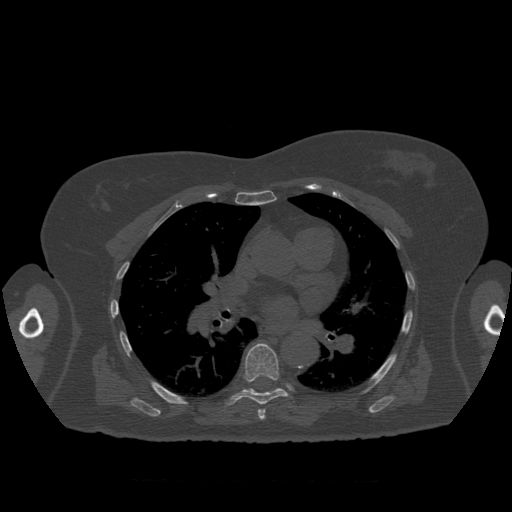
CT including the spine, one axial slice. Reconstruction kernel STANDARD. 120 kVp. Bone window (W 1800 / L 400 HU). 1.25 mm slice thickness. 512 × 512 image matrix. Patient age 81 years. From the clinical record (not read from this slice): primary cancer: renal; vertebrae with lytic lesions (as recorded): L1.
Structures marked on this image (semi-automatically segmented with operator editing):
- T7 vertebra: box from (x=225, y=343) to (x=289, y=420) px